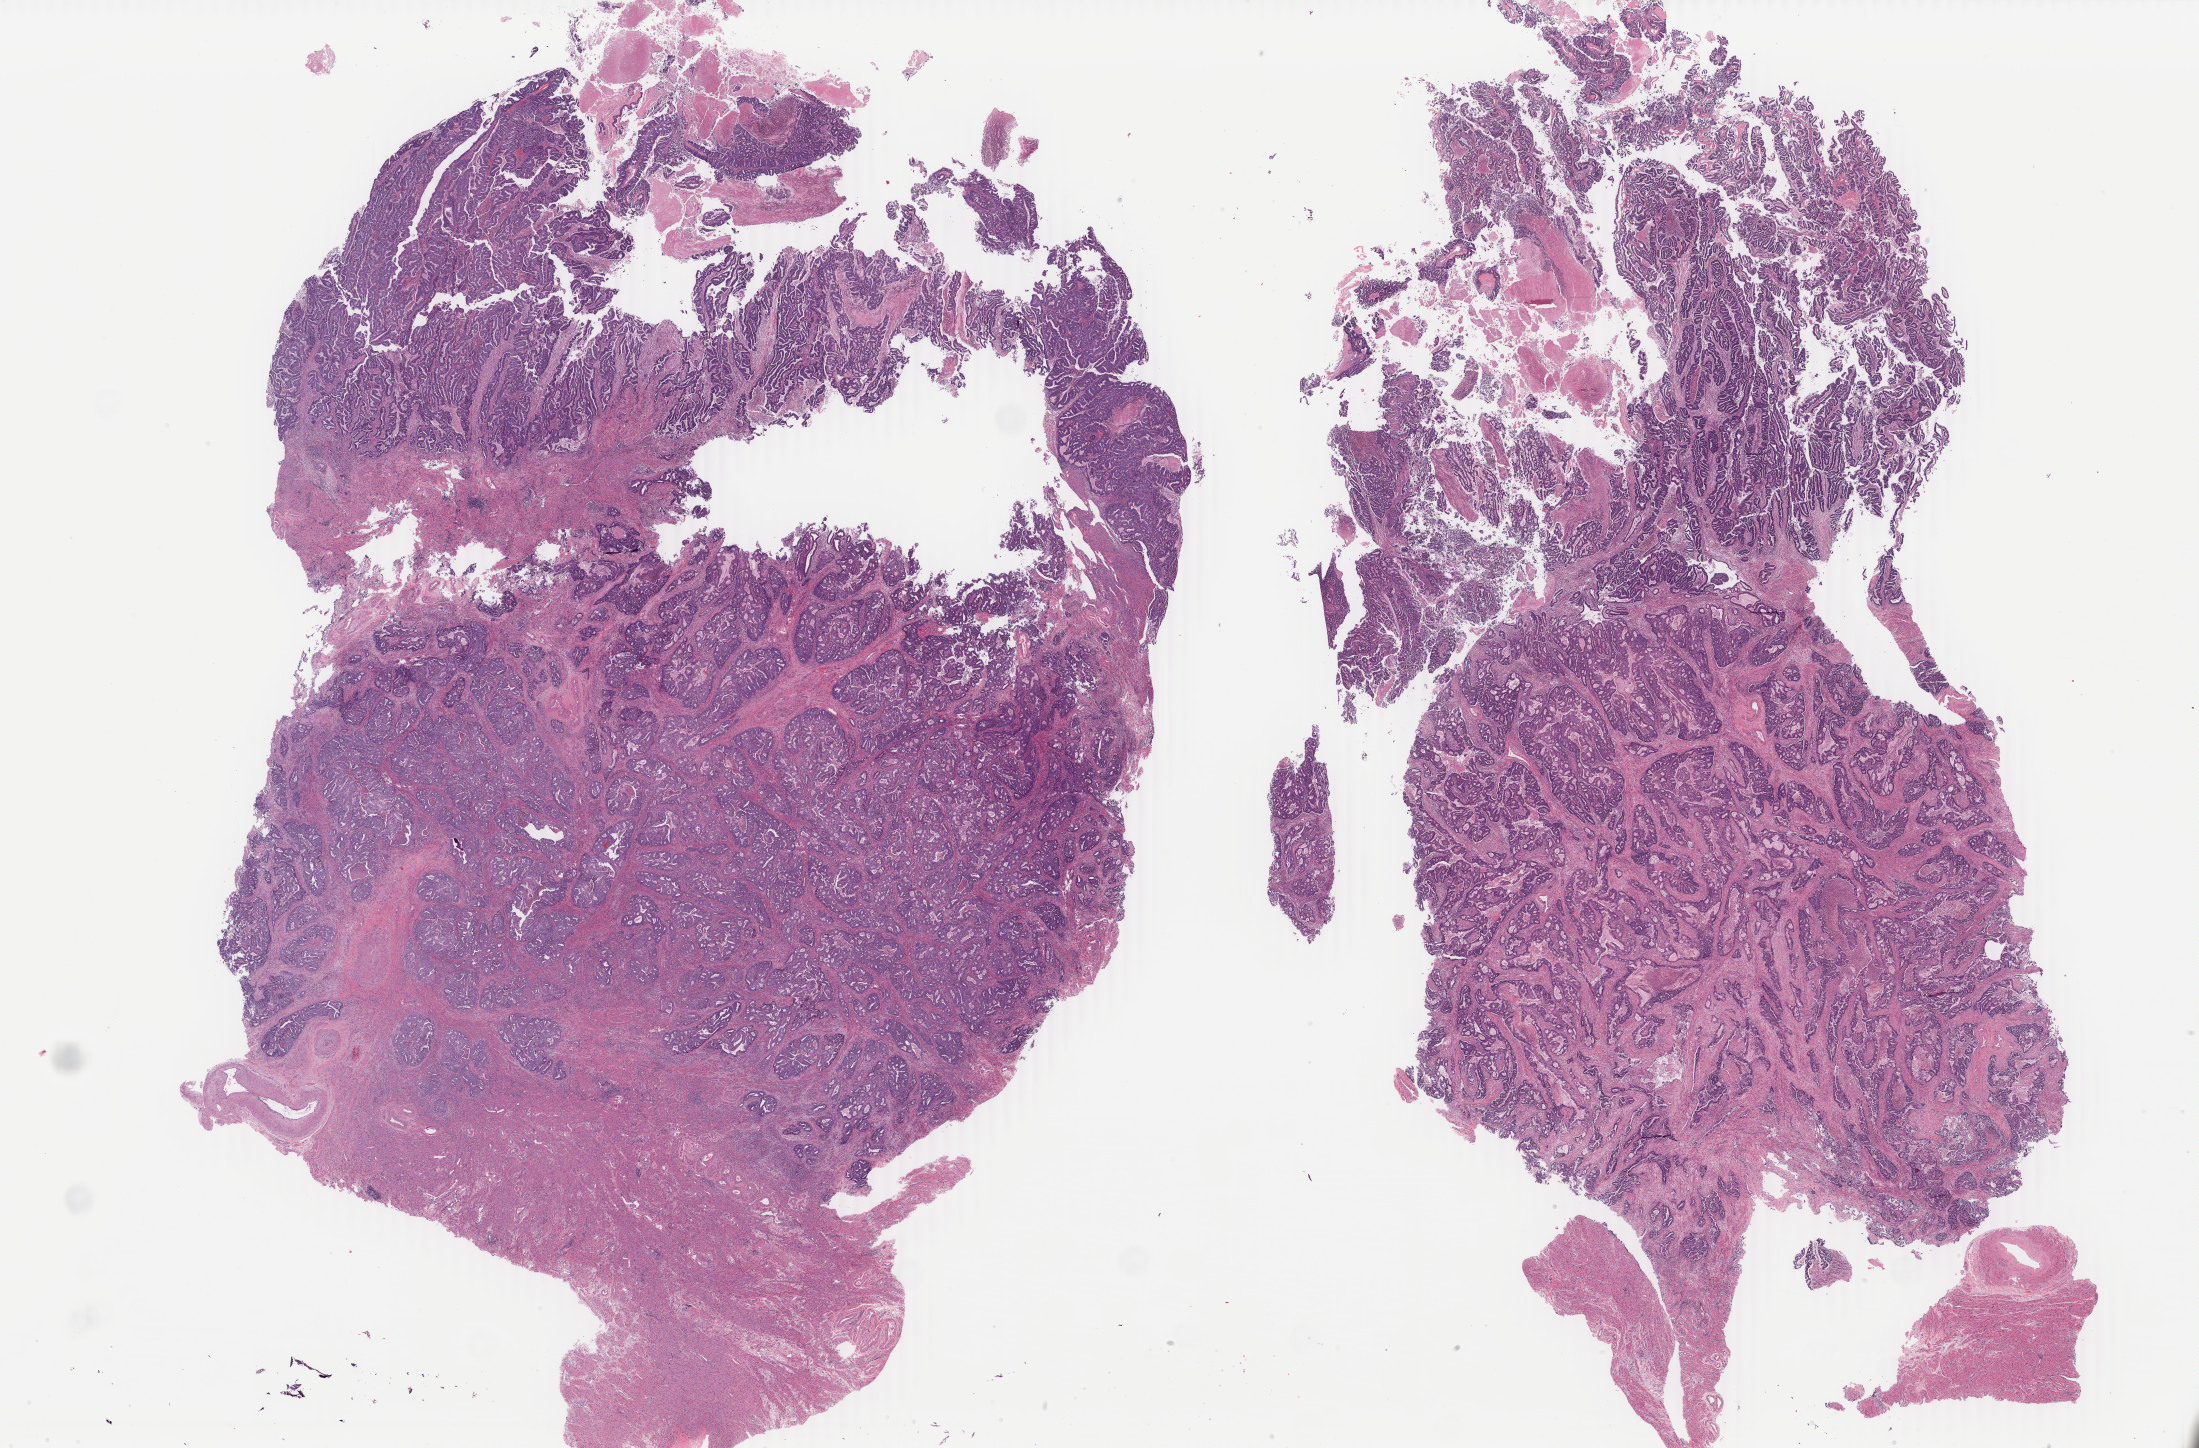
H&E whole-slide image, whole scanned area (about 35.0 x 23.0 mm, acquisition: 40x scan) shown as a low-resolution overview. FFPE section. Sample: primary tumour, uterus. Female, age 70 years at initial diagnosis. Histologic grade: G2 (moderately differentiated).
* histologic diagnosis: Endometrioid adenocarcinoma, NOS (endometrium)
* FIGO stage: IB